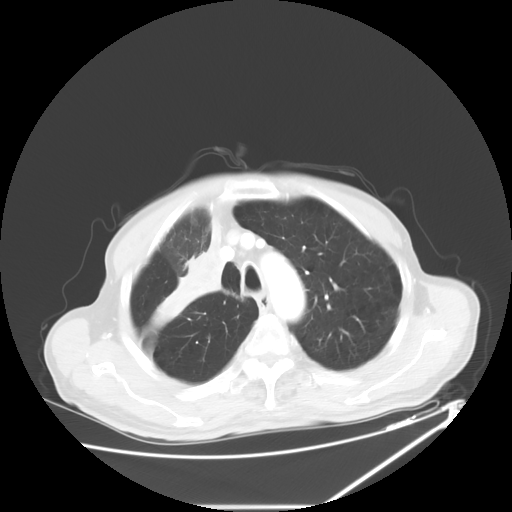
Chest CT, one axial slice. Slice 48 of 60 in the series (ordered by position). Reconstruction kernel STANDARD. Lung window (W 1500 / L -600 HU). 5 mm slice thickness. 512 × 512 image matrix. Patient: male, 73 years. Case-level facts recorded for this patient, not image findings: clinical TNM (as recorded): T2a N1 M0.
Structures marked on this image (rectangle marked by the reading radiologist):
- lung tumour (recorded histology: squamous cell carcinoma): bounding box <153,204,225,327> (left, top, right, bottom; pixels)